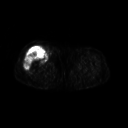
FDG PET of an extremity soft-tissue mass (from a PET/CT study), one axial slice. Position 238 of 311 along the scan axis. 3.27 mm slice thickness. 128 × 128 image matrix, field of view 500 × 500 mm. Patient: female, 57 years. From the clinical record (not read from this slice): histological type: pleiomorphic undifferentiated sarcoma; grade: high; site of the primary tumour: right quadricep.
Structures marked on this image (expert contour drawn on MRI and transferred to this co-registered scan by the dataset authors):
- tumour plus oedema (research contour): bounding box [x1, y1, x2, y2] px = [24, 48, 47, 70]
- tumour (research contour): [24, 48, 47, 70]